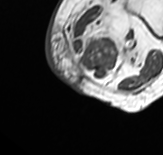
MRI of an extremity soft-tissue mass, one axial slice. Position 4 of 65 along the scan axis. MR volume resampled by the dataset authors to the PET/CT grid (not the native acquisition matrix). 3.27 mm slice thickness. 163 × 155 image matrix, field of view 159 × 151 mm. Female patient. From the clinical record (not read from this slice): histological type: pleomorphic leiomyosarcoma; grade: high; site of the primary tumour: left thigh.
Annotated regions visible in this slice (expert contour drawn on MRI and transferred to this co-registered scan by the dataset authors):
- gross tumour volume including surrounding oedema: bounding box <69,1,145,77> (left, top, right, bottom; pixels)